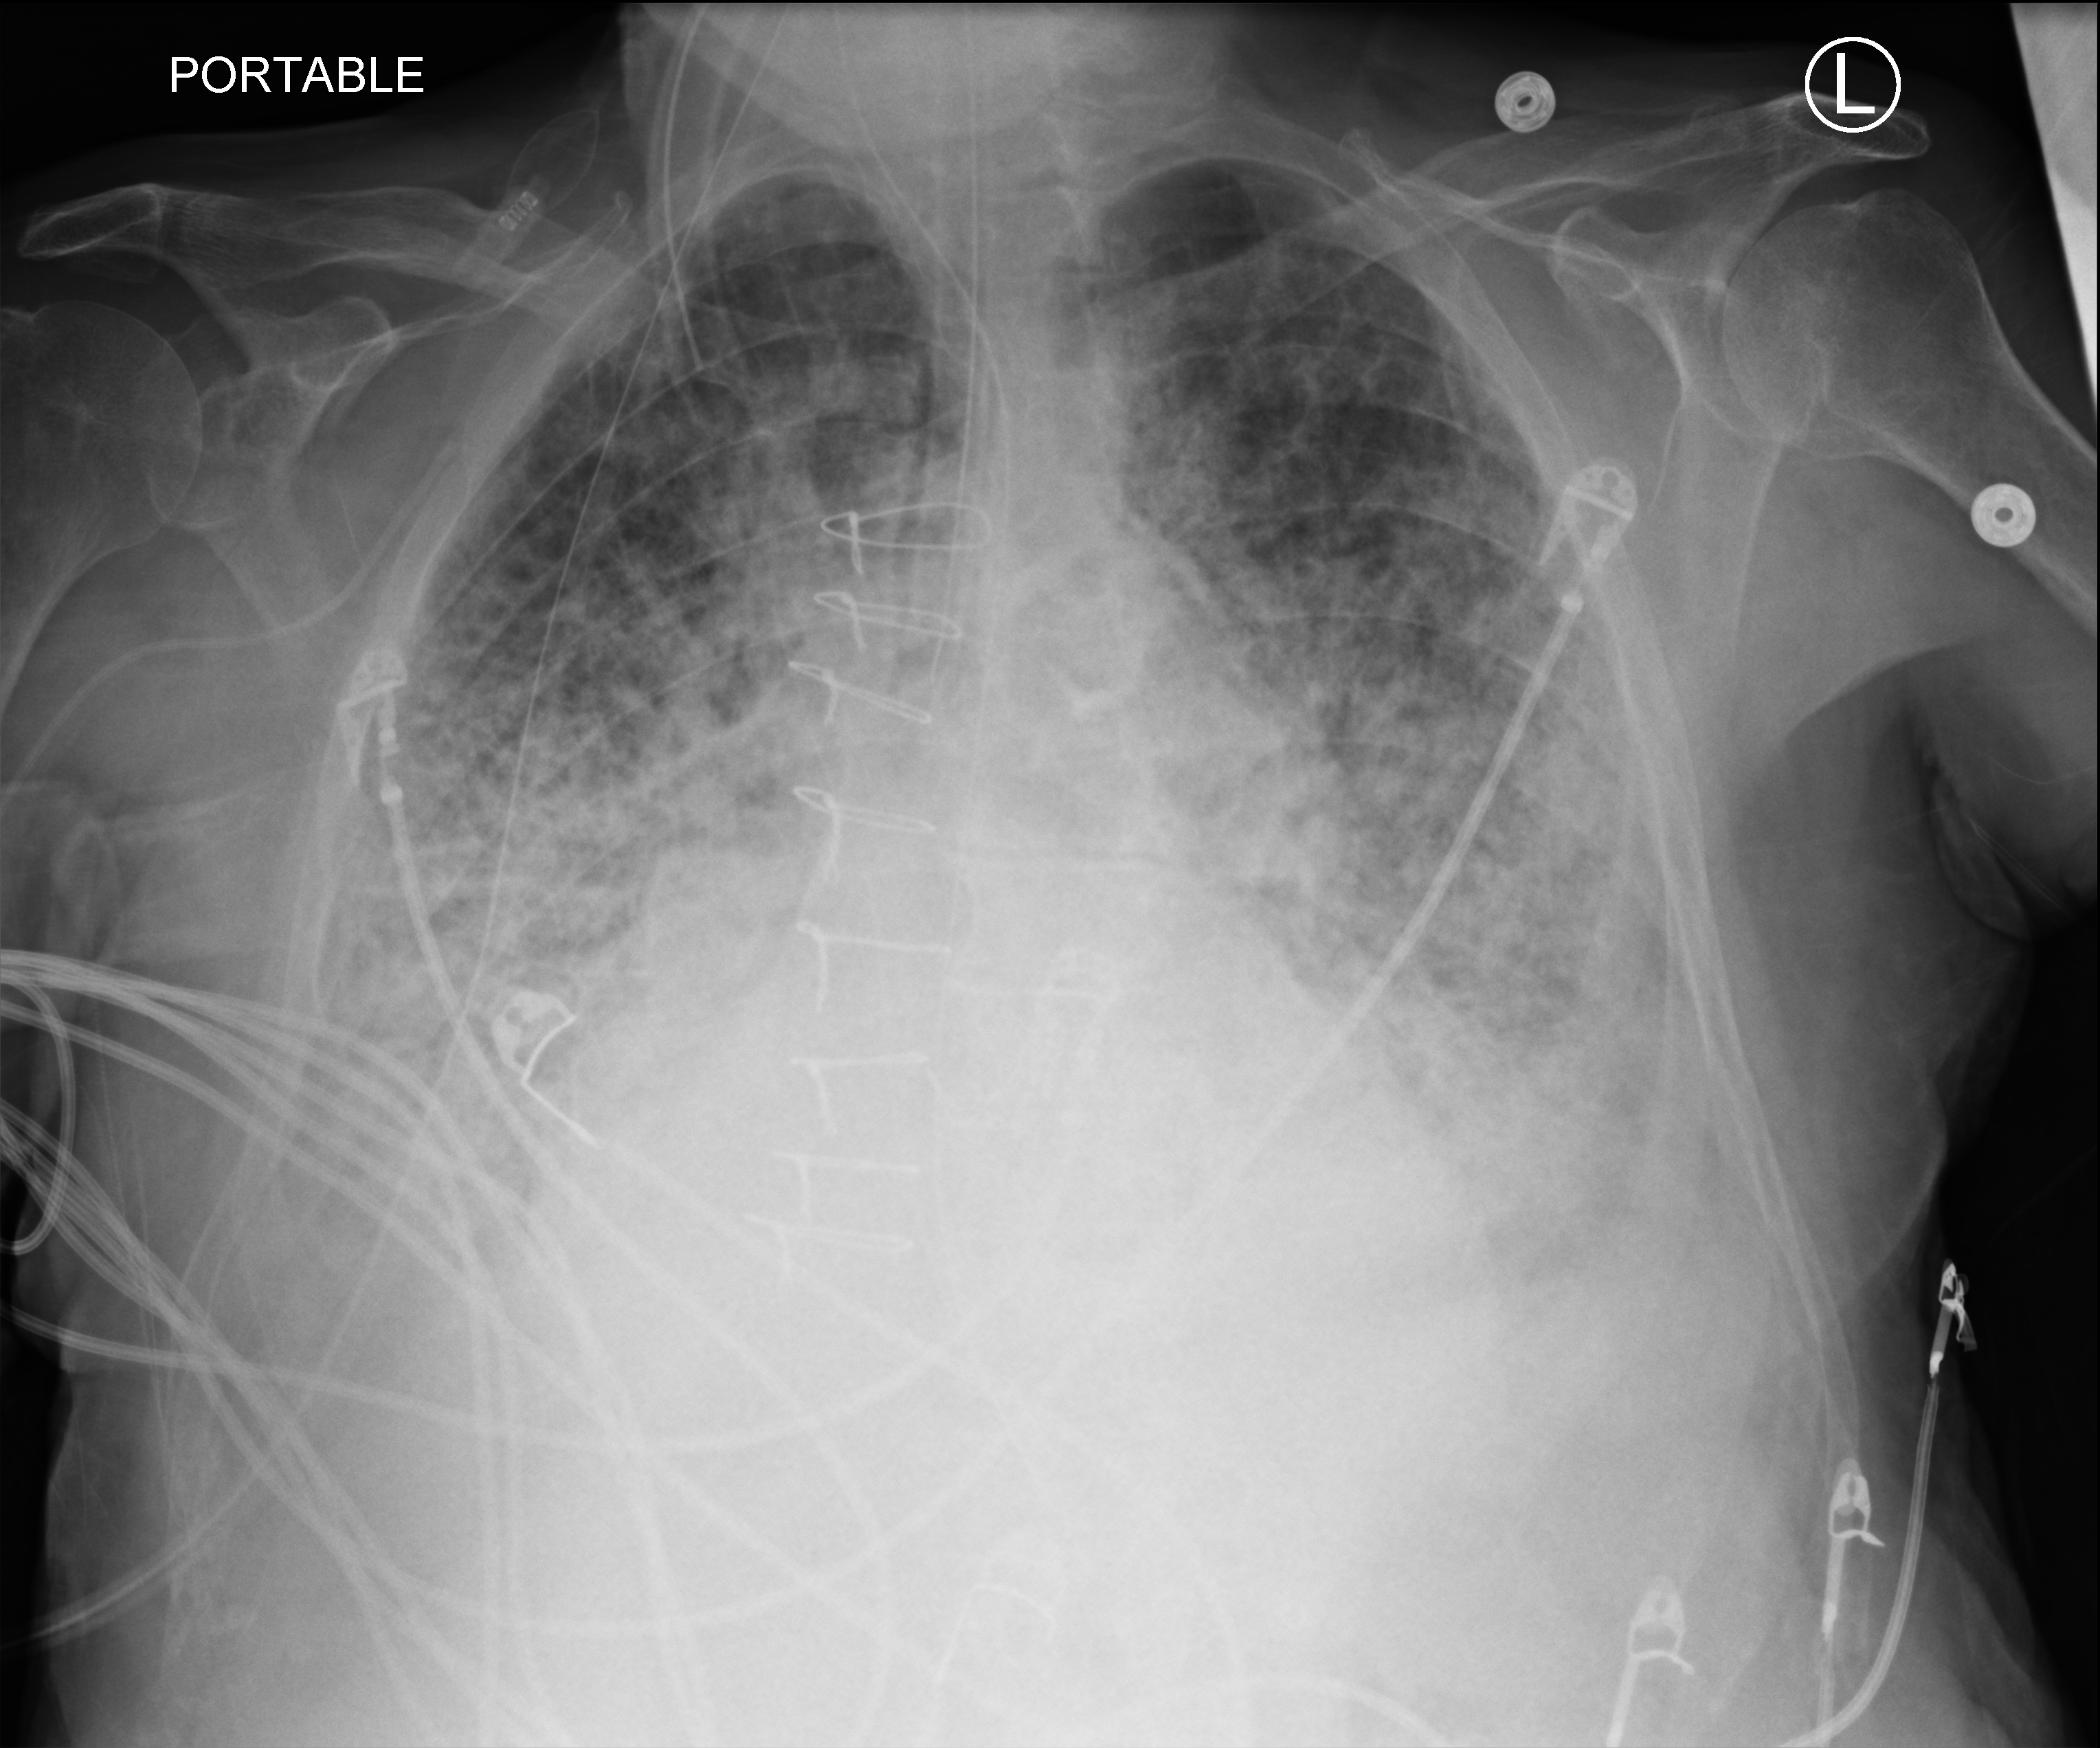
Chest X-ray (portable), anteroposterior (AP) projection. Male patient hospitalised with COVID-19, age 75–90 years.
Hospital-stay facts (about this admission, not read from this image; timing relative to this image not recorded): mechanically ventilated during this hospital stay: yes; admitted to intensive care during this hospital stay: yes.